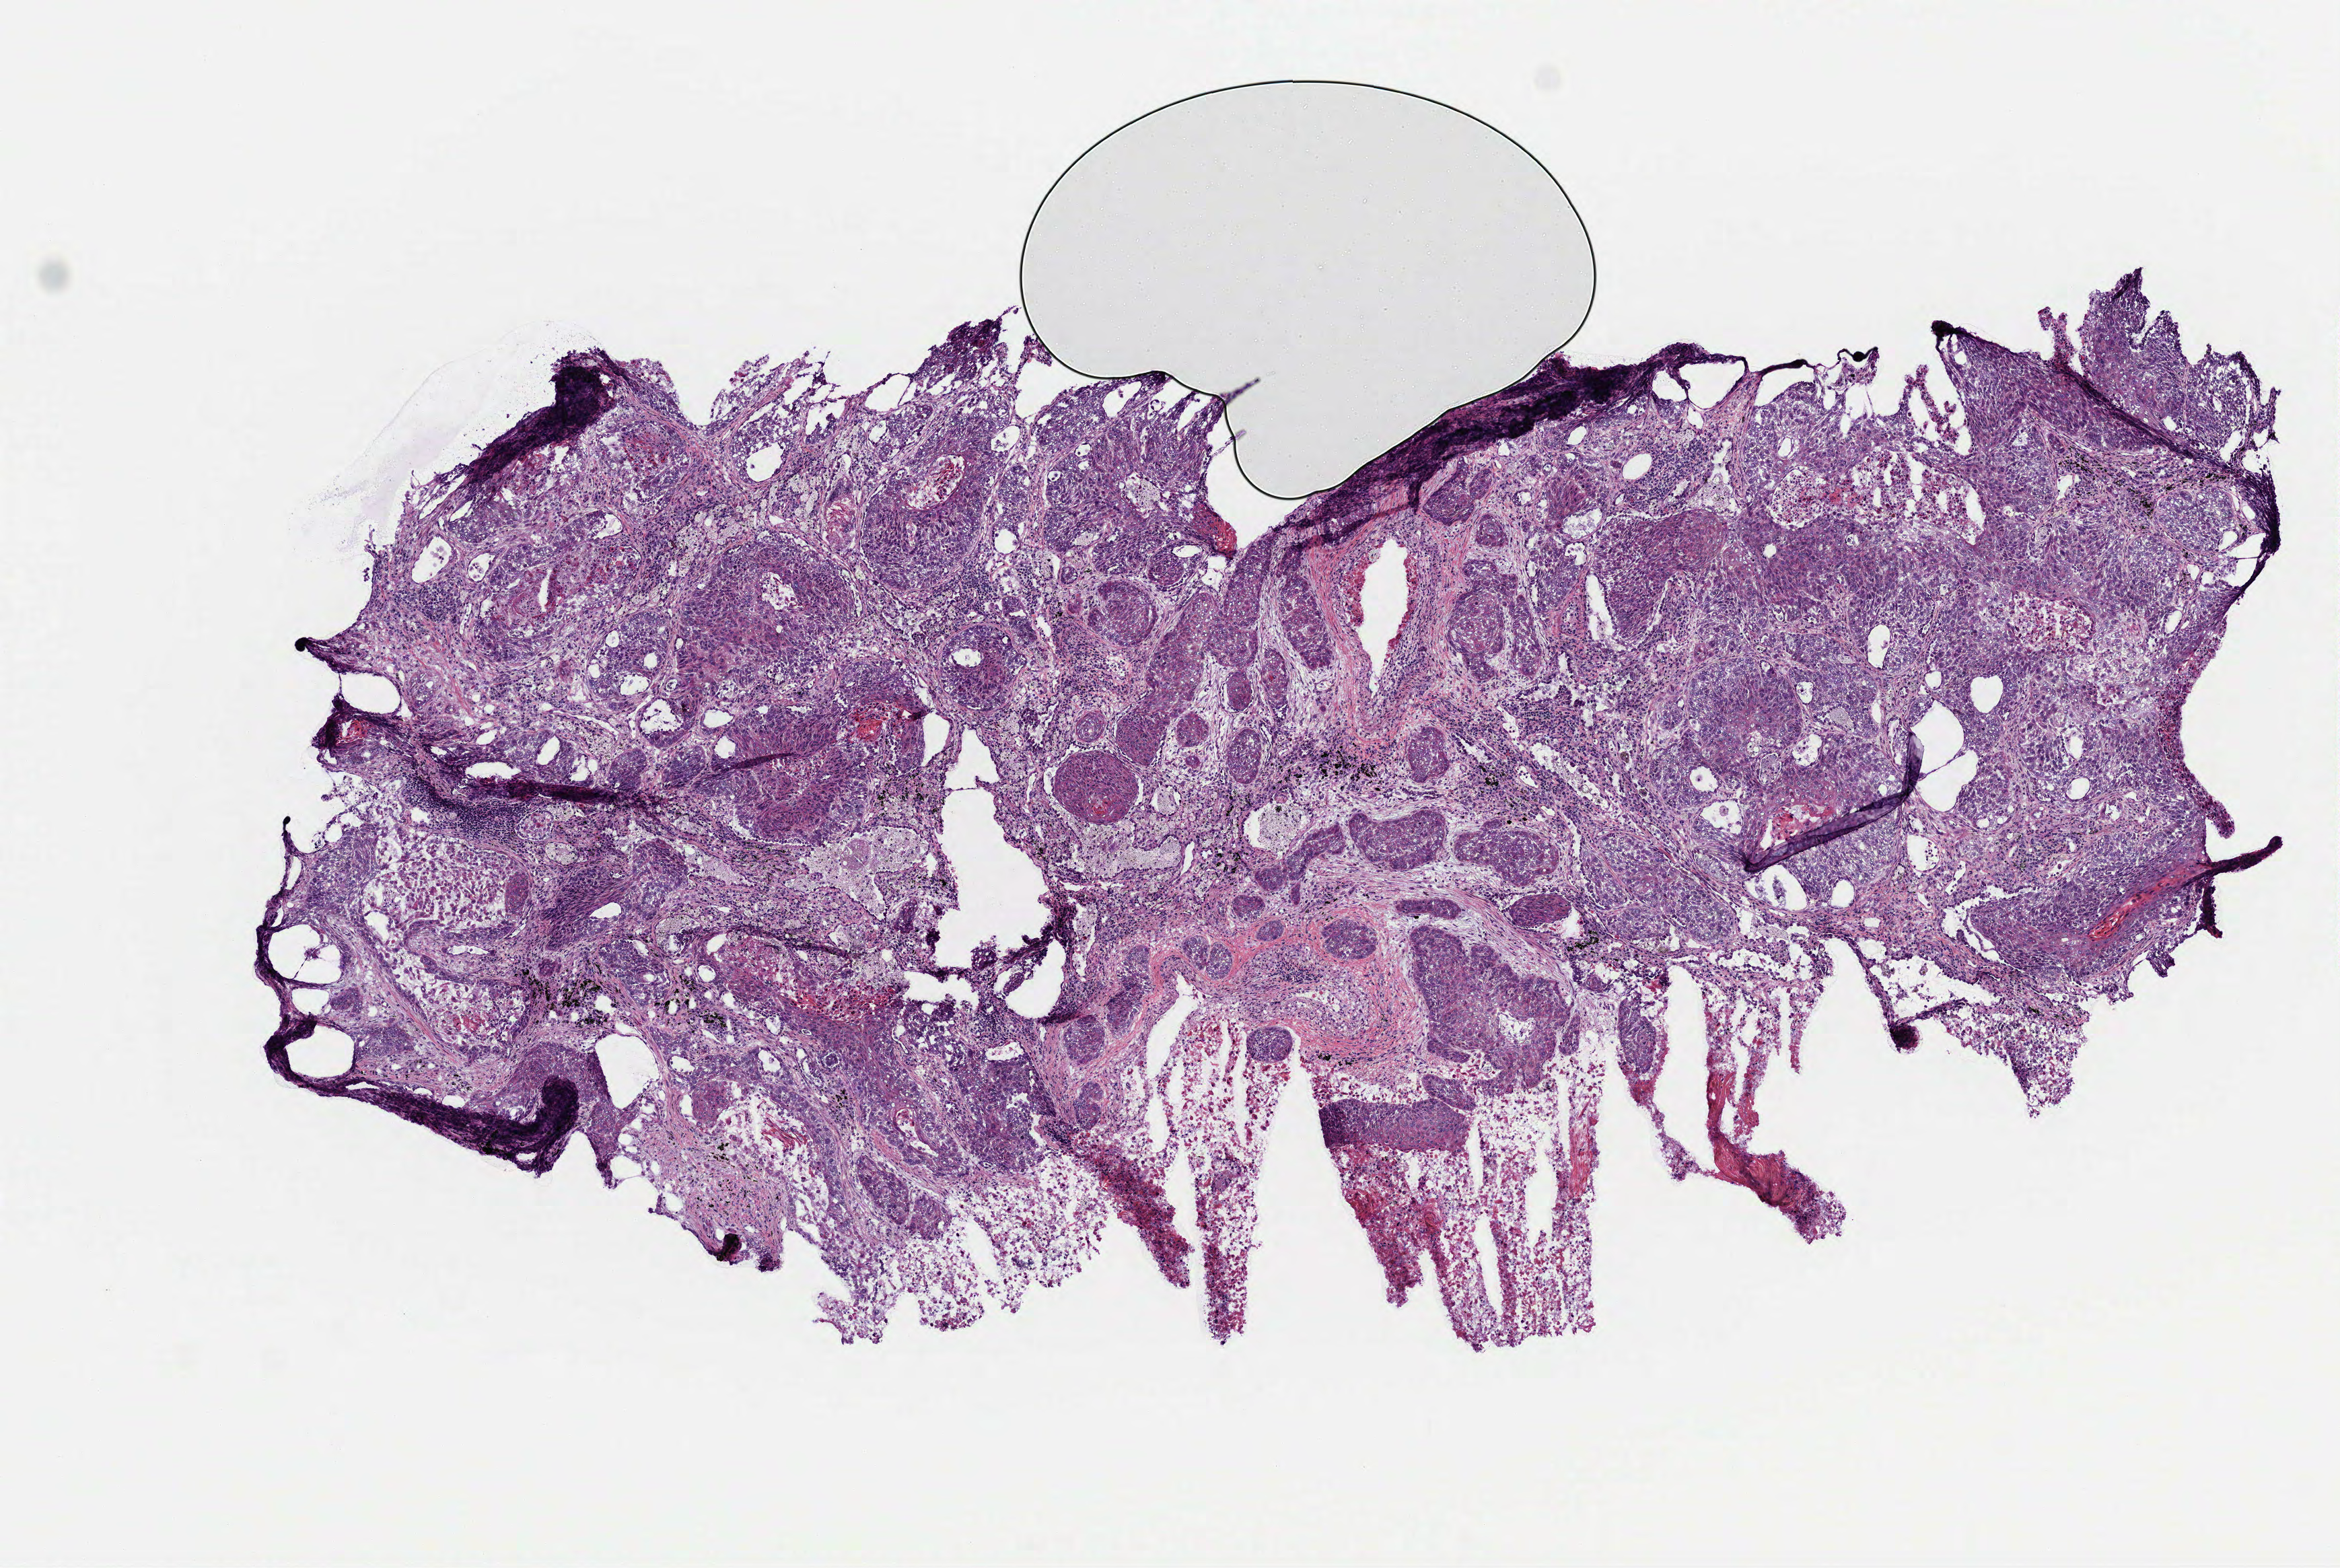
Digitized H&E tissue section (whole slide) — low-resolution overview of the scanned area, about 7.0 x 4.7 mm. Frozen section from the top of the tissue portion. Sample: primary tumour, lung. Patient: male, age at initial diagnosis 64 years. Slide review estimates, as recorded: tumour cells 100%, tumour nuclei 70%, normal cells 0%, stromal cells 0%, necrosis 0%. Infiltration values recorded for this section: lymphocyte infiltration 15%, monocyte infiltration 5%, neutrophil infiltration 0%.
* pathologic diagnosis: Squamous cell carcinoma, NOS (upper lobe, lung)
* AJCC pathologic stage: IB (6th edition)